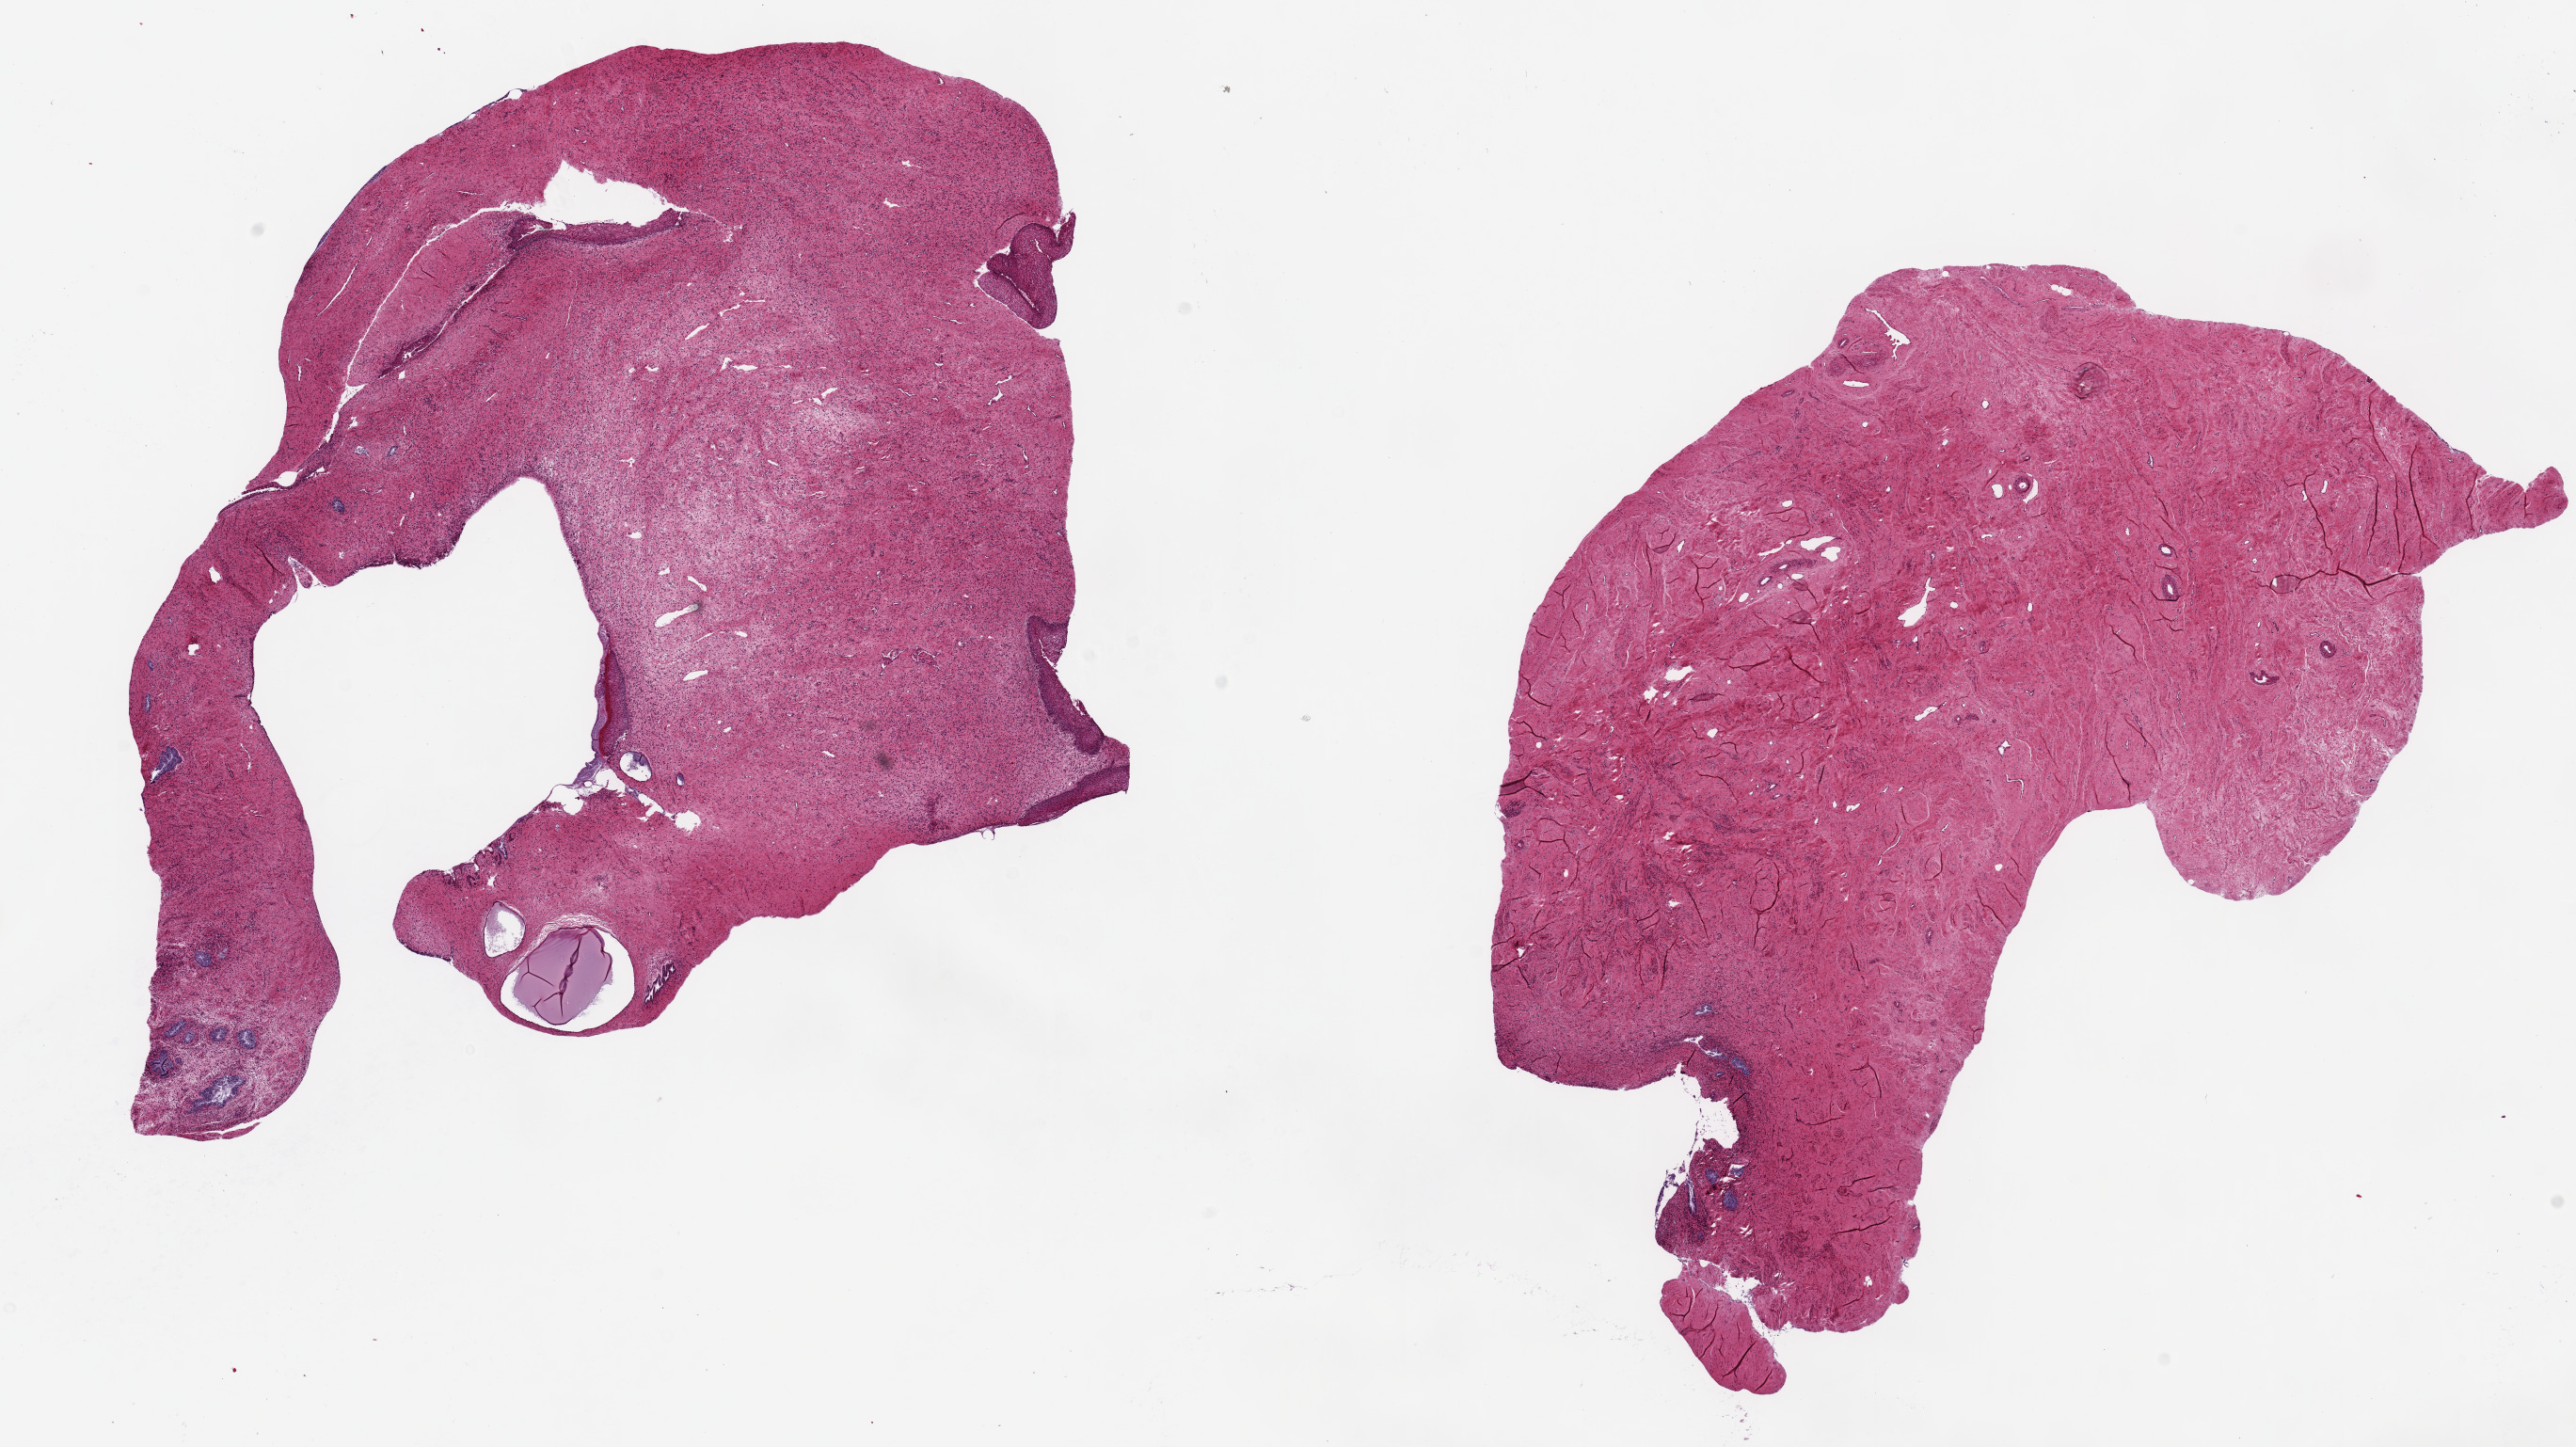
Digitized H&E-stained section, a low-resolution overview of the entire scanned area, about 21.7 x 12.2 mm (acquisition: 20x scan), PAXgene-fixed paraffin-embedded (PFPE) section, sampled site (target tissue): uterus, donor tissue sample.
- pathologist's review note for this sample: 2 pieces, 9x9 & 10x6mm; not uterus, endo/ectocervix/stroma